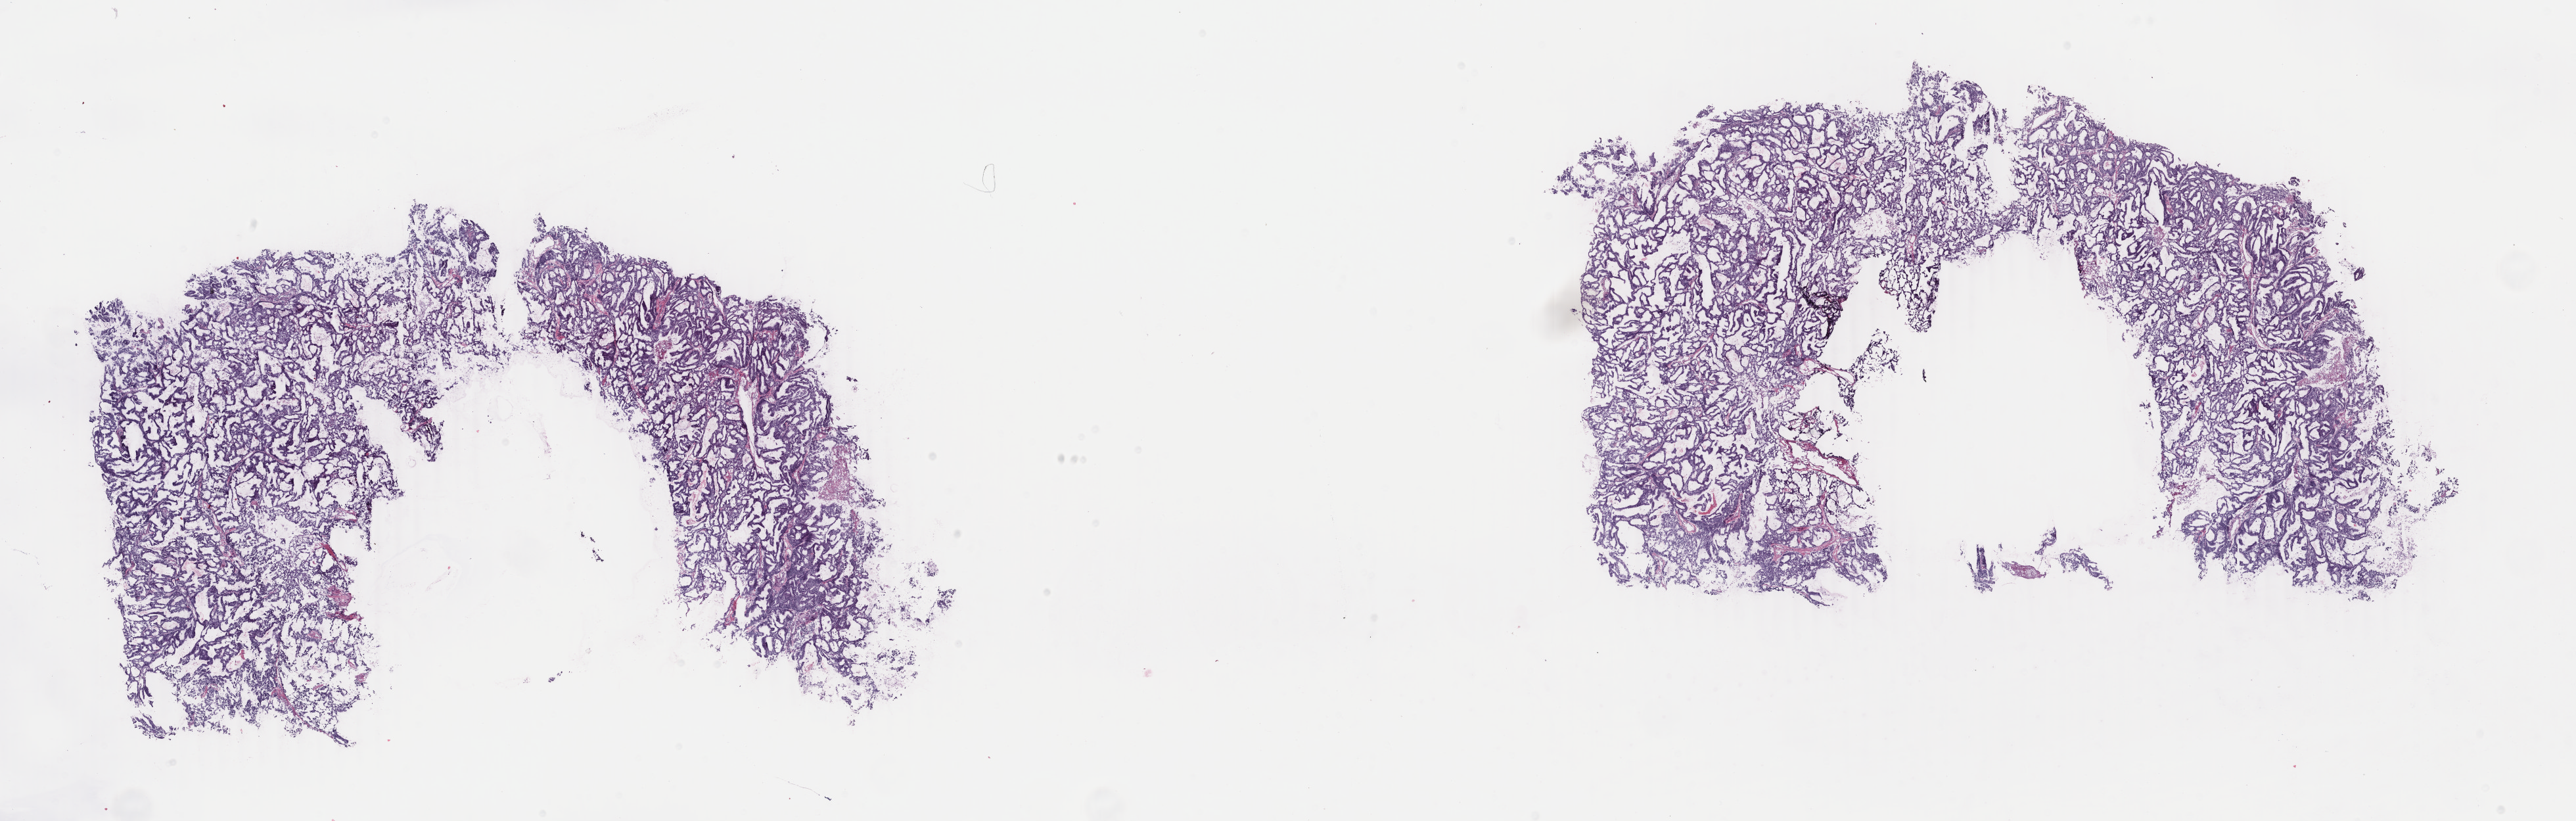
Whole-slide histology image, Hematoxylin and eosin (H&E) stained, a low-resolution overview of the entire scanned area, about 31.2 x 9.9 mm; frozen section from the top of the tissue portion; uterus, primary tumour sample. Female patient; age at initial diagnosis 78 years. Histologic grade: G1 (well differentiated). Composition of this section per pathologist review: tumour cells 92%, tumour nuclei 94%, normal cells 0%, stromal cells 6%, necrosis 2%. Inflammatory infiltration, as recorded: lymphocyte infiltration 2%, monocyte infiltration 1%, neutrophil infiltration 1%.
FIGO stage: IIIA. Lymph nodes positive (case pathology): 0 of 8 examined. Histologic diagnosis: Endometrioid adenocarcinoma, NOS (endometrium).